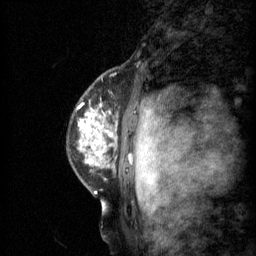
Breast MRI (dynamic contrast-enhanced), one sagittal slice. Slice 48 of 60 in the series (ordered by position). 3 images stored at this slice position (order not interpretable as contrast timing). 1.5 T. TE 4.2 ms, TR 11 ms. 2 mm slice thickness. 256 × 256 image matrix, field of view 200 × 200 mm. Patient: female, 48 years.
Structures marked on this image (semi-automatically segmented with operator editing):
- analysis volume of interest (the breast-tissue region the enhancement analysis was run in; not a lesion): box from (x=79, y=76) to (x=139, y=147) px
- tumour enhancement mask (voxels above the 70 % enhancement threshold inside the analysis volume of interest): (x=81, y=114)–(x=114, y=145)